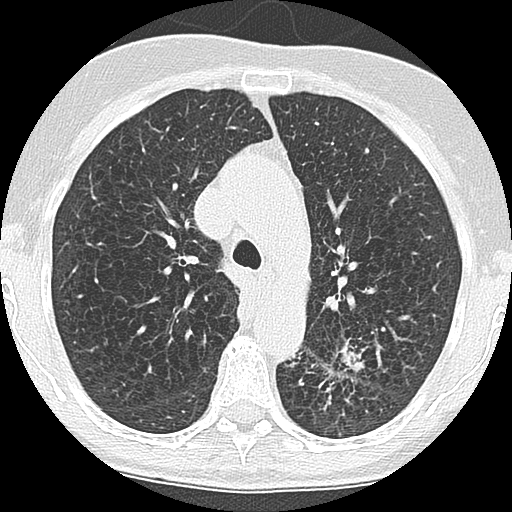
Low-dose screening chest CT, one axial slice. Slice 122 of 171 in the series (ordered by position). 120 kVp. Lung window (W 1500 / L -600 HU). 512 × 512 image matrix, field of view 280 × 280 mm.
Outlined on this slice (outlined manually by an expert reader):
- lesion 1 (tumor, lower lobe of left lung): bounding box <336,343,366,371> (left, top, right, bottom; pixels)